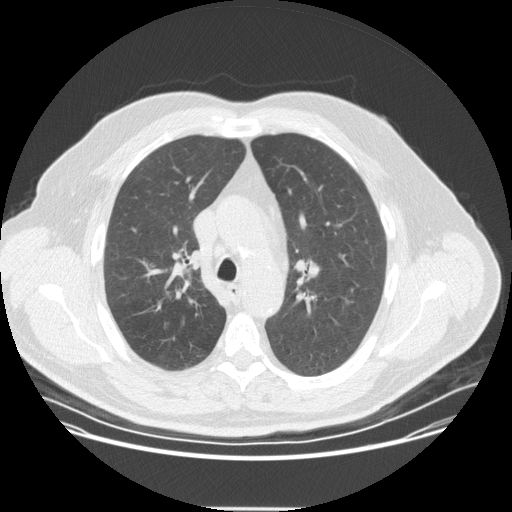
Axial slice from a low-dose chest CT screening exam, second screening round (one year after baseline), lung window (W 1500 / L -600 HU), 2.5 mm slice thickness, standard (soft-tissue) reconstruction kernel (STANDARD). Male participant, aged 57 years at enrolment. Current smoker at enrolment.
- Expert-annotated lung lesion, box from (x=143, y=247) to (x=211, y=315) px.
- Screening reader's record for this exam (one nodule recorded; not confirmed to be the boxed lesion): non-calcified nodule or mass ≥4 mm, right upper lobe, 20 × 16 mm, spiculated (stellate) margins, soft tissue attenuation, pre-existing on the prior screen: no.
- Official screen result: positive, other.
- Later outcome: lung cancer diagnosed 35 days after this screen — non-small cell carcinoma, right upper lobe, poorly differentiated (G3), stage IIA (AJCC 6th edition), 25 mm at pathology.